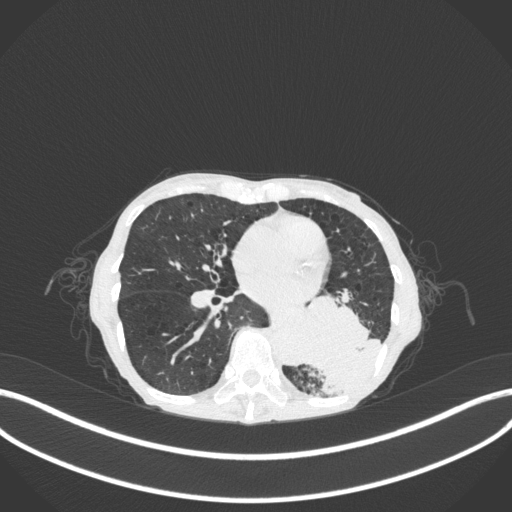
Chest CT, one axial slice. Slice 121 of 347 in the series (ordered by position). Reconstruction kernel B31f. Lung window (W 1500 / L -600 HU). 1 mm slice thickness. 512 × 512 image matrix, field of view 400 × 400 mm. Patient: female, 70 years. Case-level facts recorded for this patient, not image findings: clinical TNM (as recorded): T3 N0 M0; histopathological grade: G3.
Annotated regions visible in this slice (rectangle marked by the reading radiologist):
- lung tumour (recorded histology: small cell carcinoma): bounding box (x1, y1, x2, y2) in pixels: (294, 291, 385, 395)